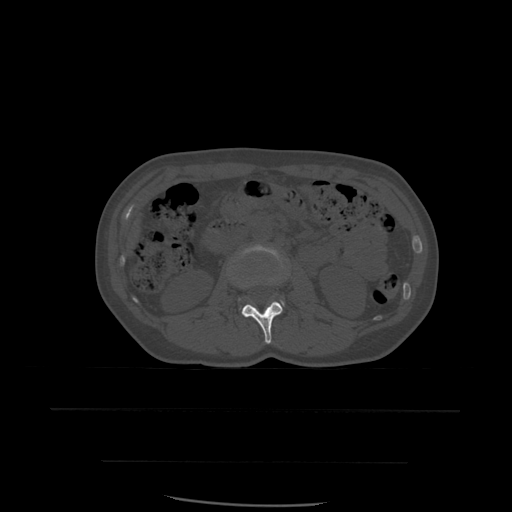
CT including the spine, one axial slice. Position 214 of 574 along the scan axis. Bone window (W 1800 / L 400 HU). 1.25 mm slice thickness. 512 × 512 image matrix, field of view 392 × 392 mm. Patient age 48 years. Case-level facts recorded for this patient, not image findings: primary cancer: lung; vertebrae with lytic lesions (as recorded): T11.
Outlined on this slice (semi-automatic segmentation, software-assisted and operator-edited):
- L2 vertebra: box from (x=241, y=302) to (x=283, y=345) px
- L3 vertebra: (x=244, y=246)–(x=285, y=306)